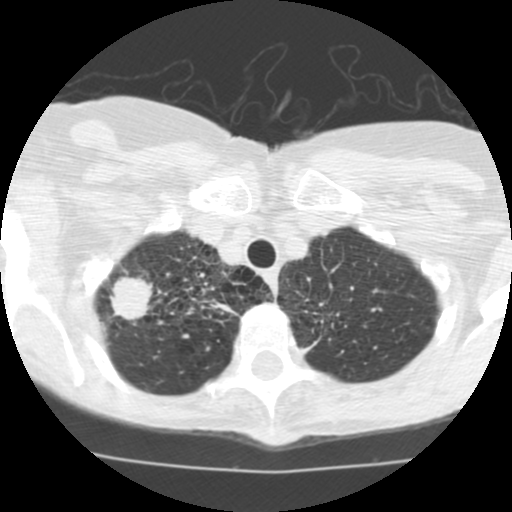
Low-dose screening chest CT, one axial slice. Slice 100 of 115 in the series (ordered by position). Lung window (W 1500 / L -600 HU). 2.5 mm slice thickness. 512 × 512 image matrix, field of view 280 × 280 mm.
Annotated regions visible in this slice (outlined manually by an expert reader):
- lesion 1 (tumor, upper lobe of right lung): bounding box (x1, y1, x2, y2) in pixels: (110, 276, 153, 320)